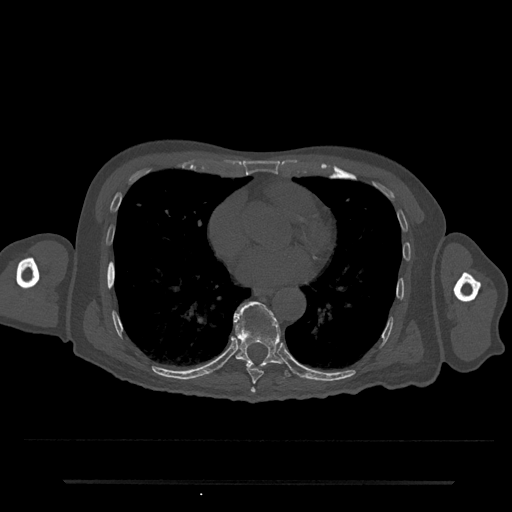
CT including the spine, one axial slice. Slice 393 of 797 in the series (ordered by position). 120 kVp. Bone window (W 1800 / L 400 HU). 0.5 mm slice thickness. 512 × 512 image matrix, field of view 427 × 427 mm. Patient: male, 74 years. From the clinical record (not read from this slice): primary cancer: prostate.
Annotated regions visible in this slice (semi-automatically segmented with operator editing):
- T7 vertebra: bounding box [x1, y1, x2, y2] px = [250, 387, 256, 394]
- T8 vertebra: [247, 369, 264, 384]
- T9 vertebra: [233, 301, 290, 377]